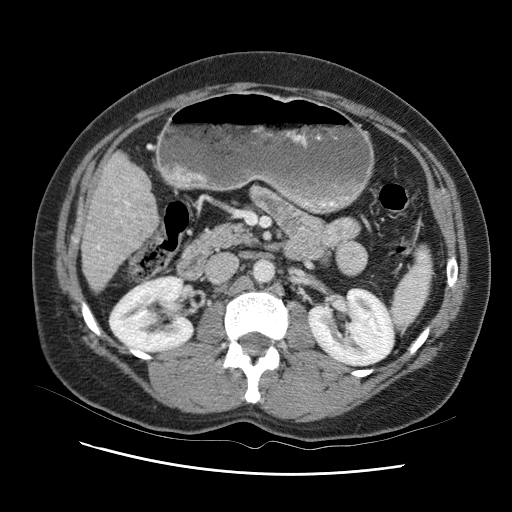
Contrast-enhanced abdominal CT (liver protocol), one axial slice. Position 33 of 95 along the scan axis. One of 2 acquisitions stored at this slice position. Soft-tissue window (W 400 / L 40 HU). 2.5 mm slice thickness. 512 × 512 image matrix, field of view 360 × 360 mm. From the clinical record (not read from this slice): diagnosis: hepatocellular carcinoma (patient treated with transarterial chemoembolisation; whether this scan precedes or follows treatment is not stated here); TNM stage (as recorded): Stage-I; Child-Pugh class: B; tumour differentiation: moderately differentiated; tumour nodularity: uninodular.
Annotated regions visible in this slice (semi-automatic segmentation, software-assisted and operator-edited):
- liver parenchyma outside the tumour (the mass and vessels are separate outlines, so this box may not span the whole liver): bounding box <82,141,166,298> (left, top, right, bottom; pixels)
- liver vessels: <98,165,144,273>